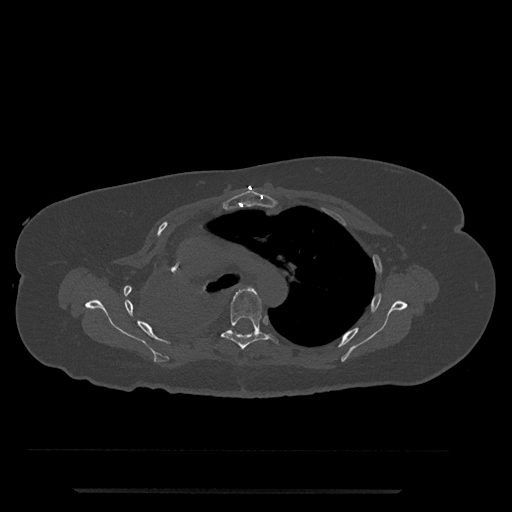
CT including the spine, one axial slice. Slice 546 of 797 in the series (ordered by position). Reconstruction kernel Br40s/3. 120 kVp. Bone window (W 1800 / L 400 HU). 512 × 512 image matrix. Patient: female, 51 years. From the clinical record (not read from this slice): primary cancer: neuro; vertebrae with lytic lesions (as recorded): T8.
Structures marked on this image (semi-automatic segmentation, software-assisted and operator-edited):
- T5 vertebra: box from (x=209, y=288) to (x=278, y=350) px